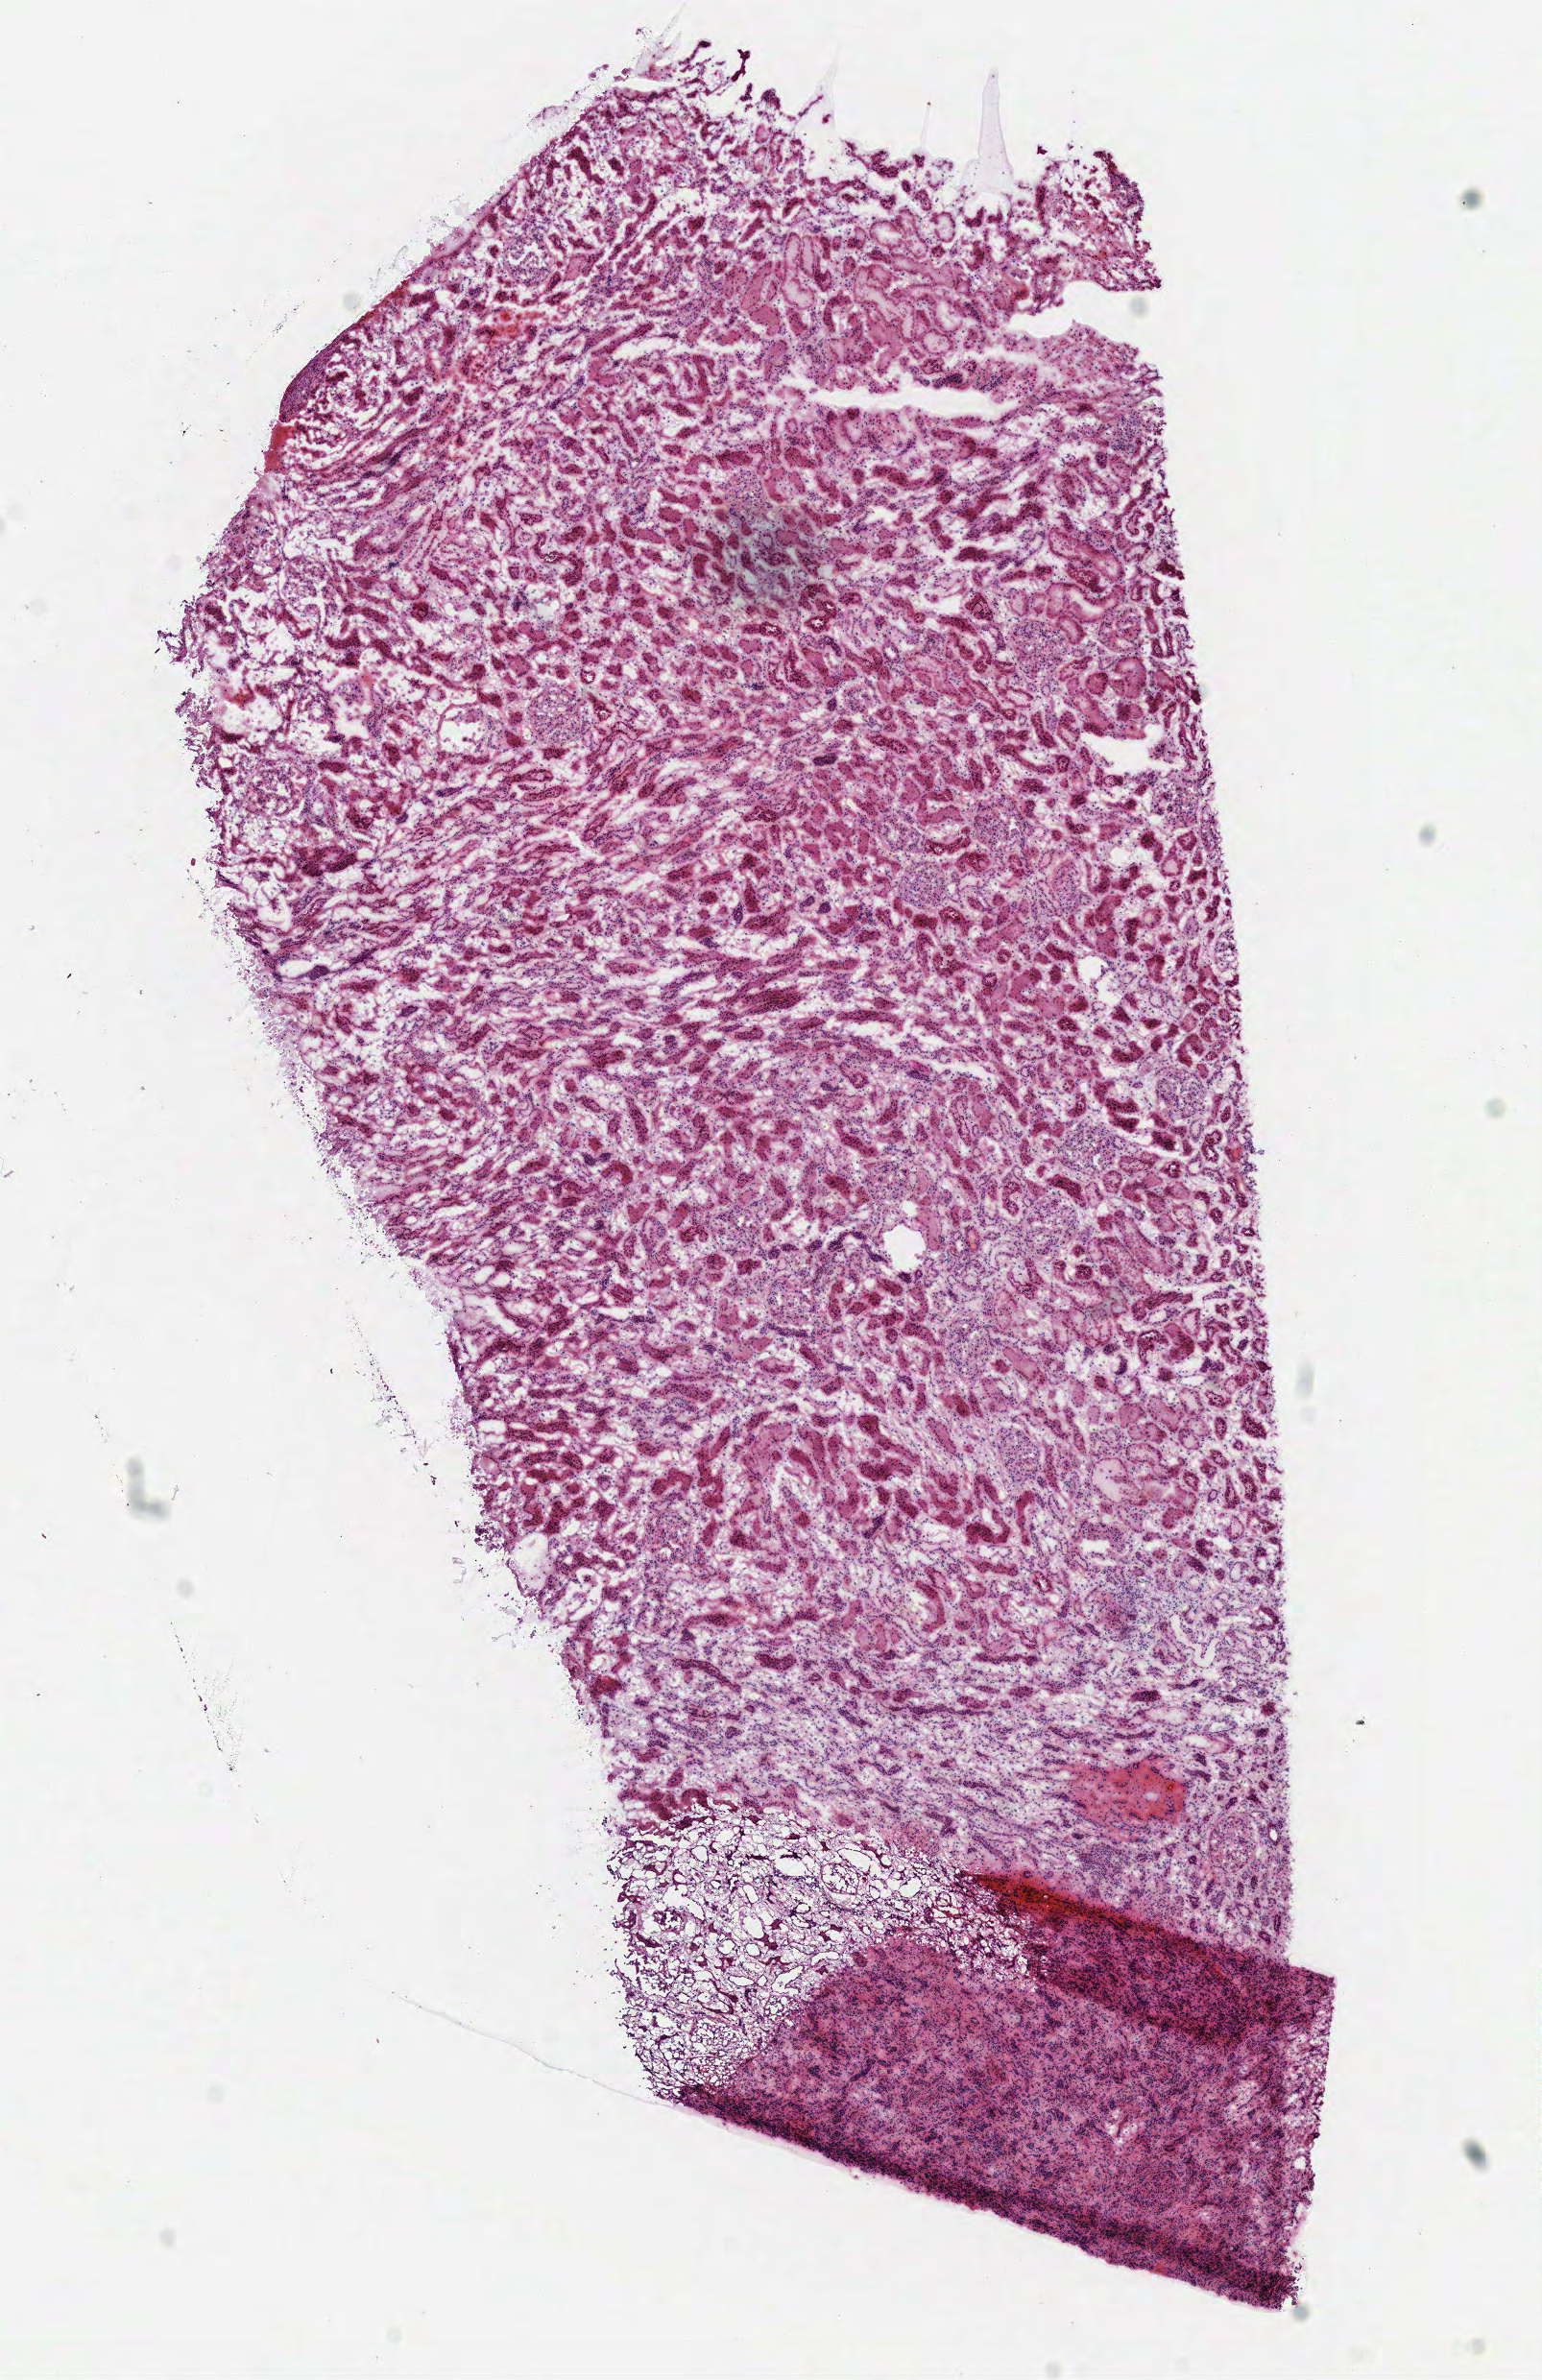
Digitized H&E-stained tissue section (whole slide), whole scanned area (about 6.3 x 9.8 mm) shown as a low-resolution overview, frozen section from the top of the tissue portion, solid tissue normal (non-tumour tissue) sample from the kidney. Female patient; age at initial diagnosis 44 years.
This section: solid tissue normal sample (biorepository sample class). Patient diagnosis: Clear cell adenocarcinoma, NOS.